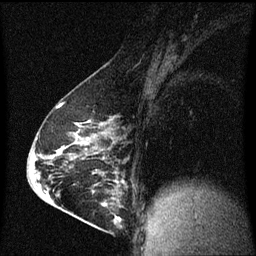
Breast MRI (dynamic contrast-enhanced), one sagittal slice; slice 36 of 60 in the series (ordered by position); dynamic contrast-enhanced series, image 2 of 3 at this slice position (ordered by acquisition); 1.5 T; TE 4.2 ms, TR 8 ms; 256 × 256 image matrix, field of view 200 × 200 mm. Patient: female, 63 years.
Structures marked on this image (semi-automatic segmentation, software-assisted and operator-edited):
- analysis volume of interest (the breast-tissue region the enhancement analysis was run in; not a lesion): bounding box <88,182,129,229> (left, top, right, bottom; pixels)
- tumour enhancement mask (voxels above the 70 % enhancement threshold inside the analysis volume of interest): <102,182,125,225>